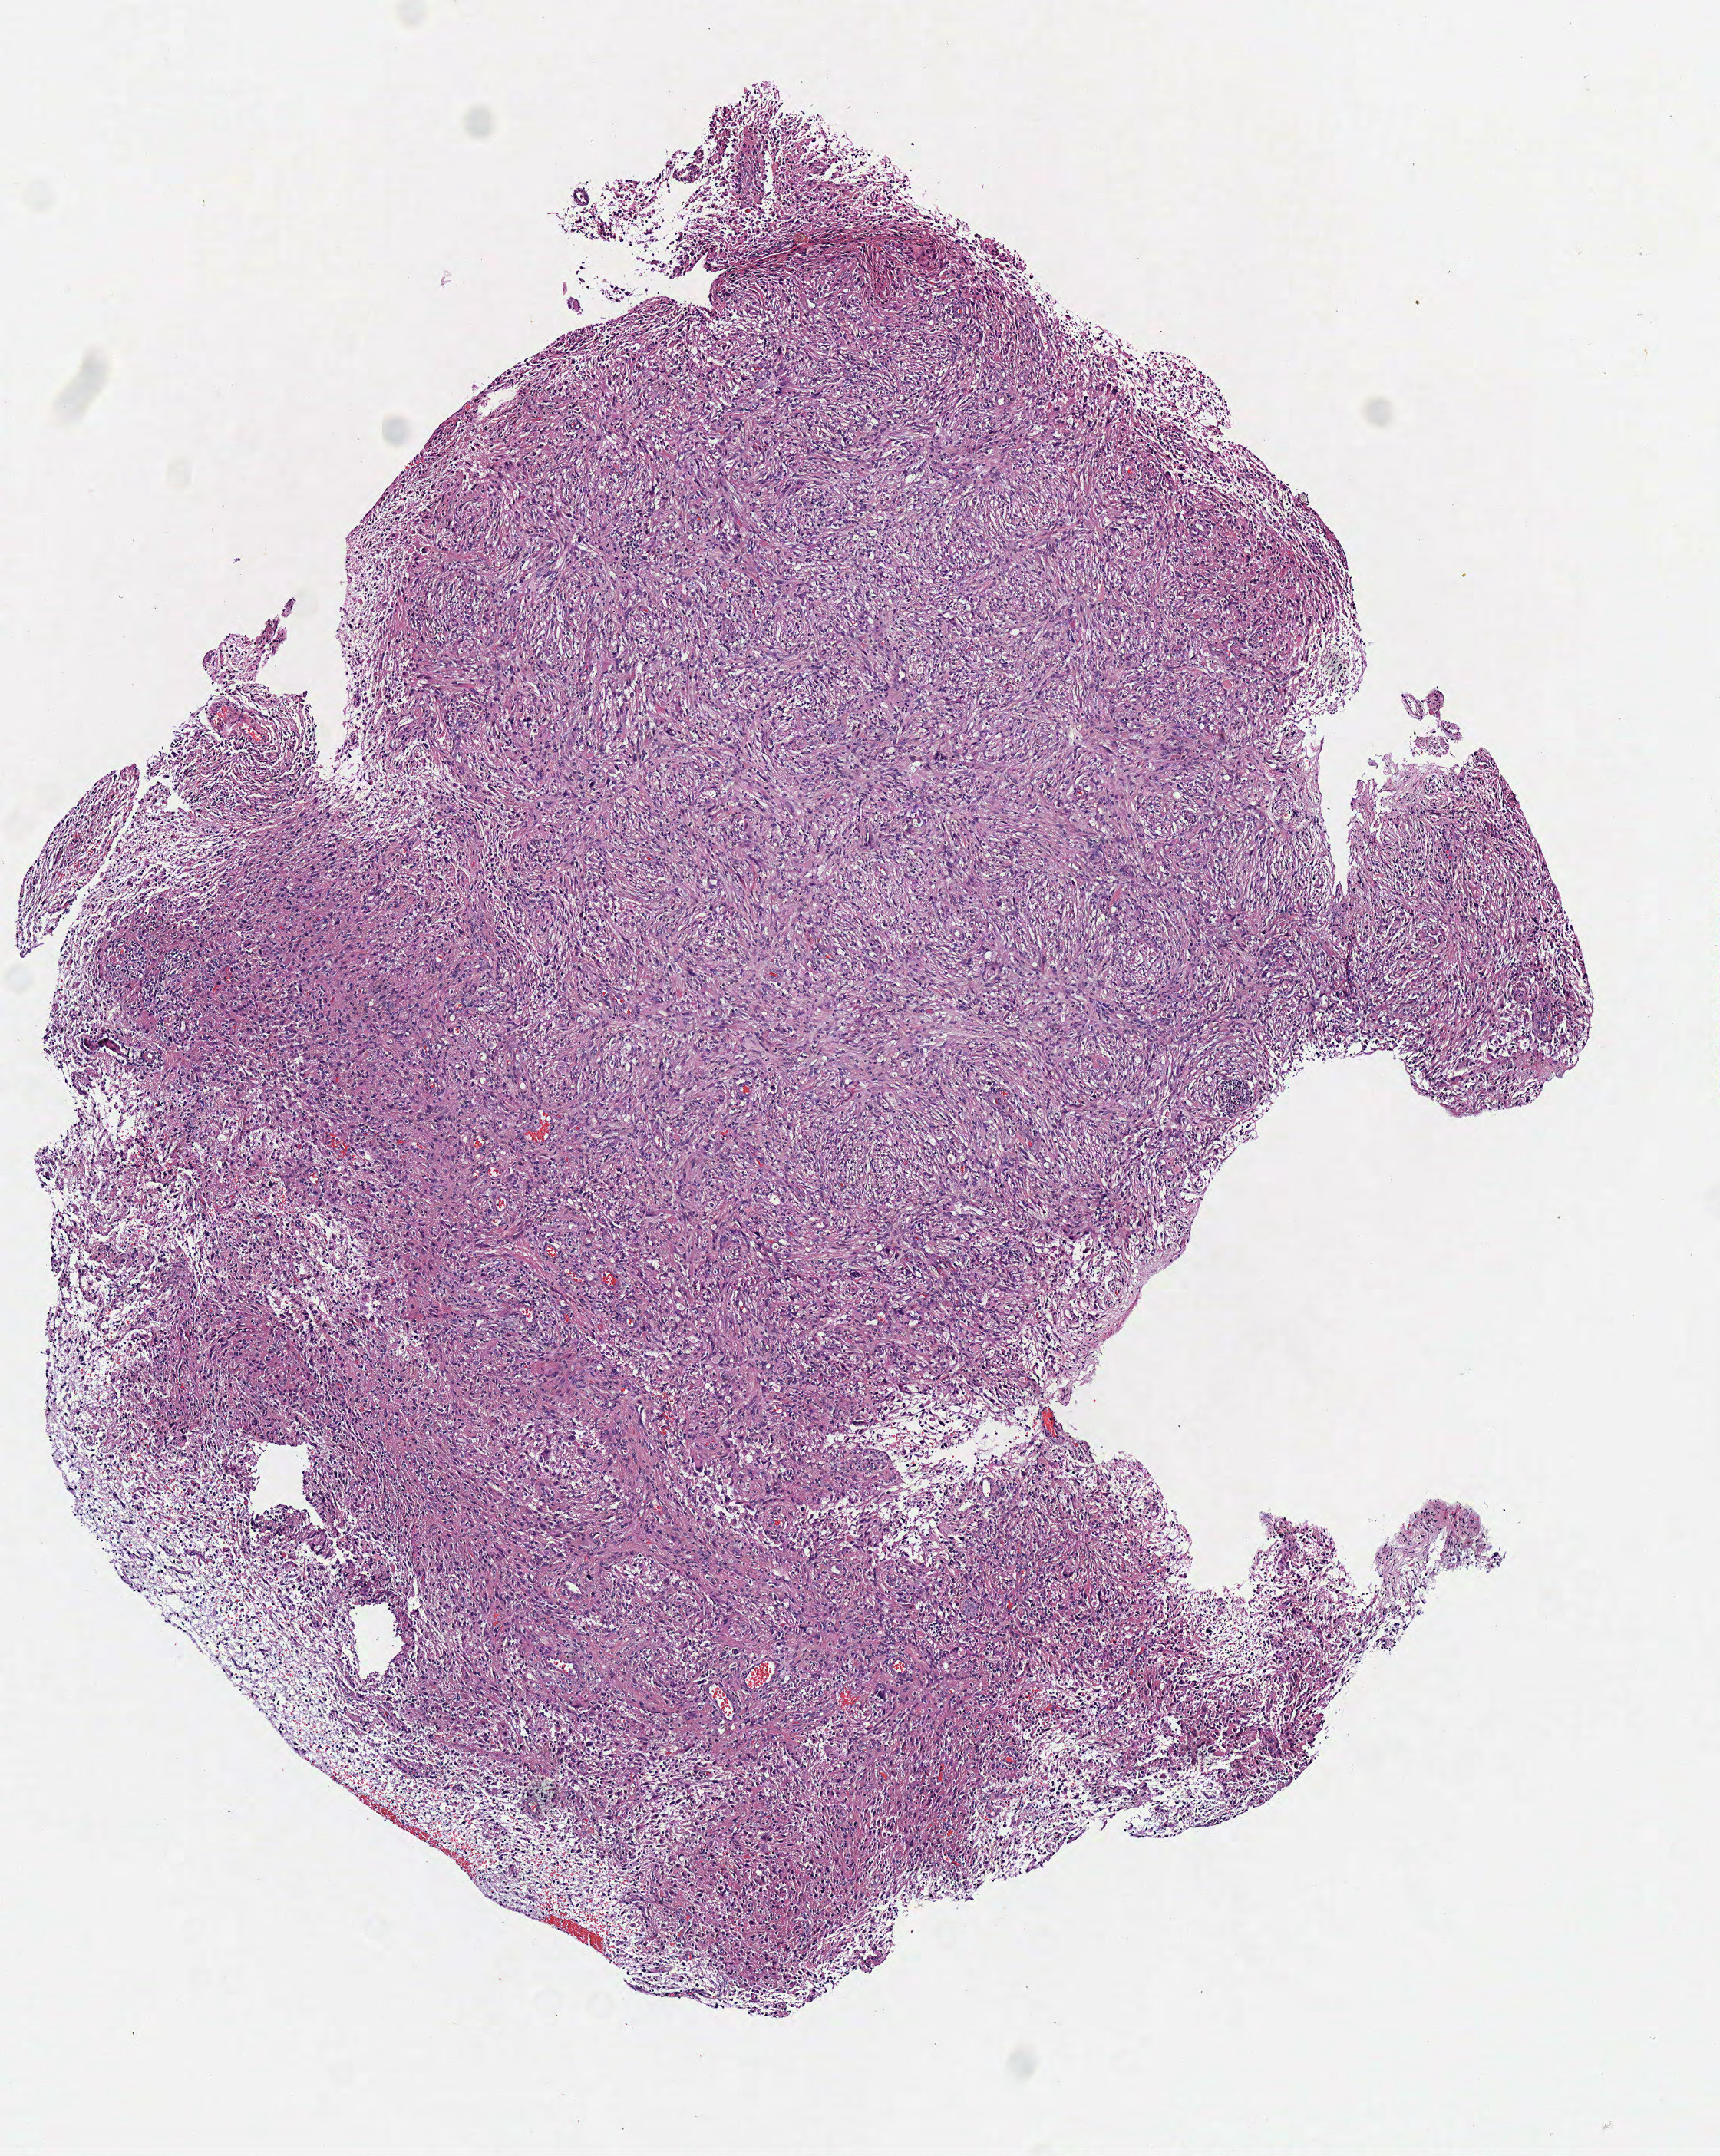
Hematoxylin and eosin (H&E) stained whole-slide image, a low-resolution overview of the entire scanned area, about 4.4 x 5.5 mm, frozen section from the top of the tissue portion, brain, primary tumour sample. Male patient; age at initial diagnosis 65 years. Slide review estimates, as recorded: tumour cells 100%, tumour nuclei 80%, normal cells 0%, stromal cells 0%, necrosis 0%.
Diagnosis: Glioblastoma.